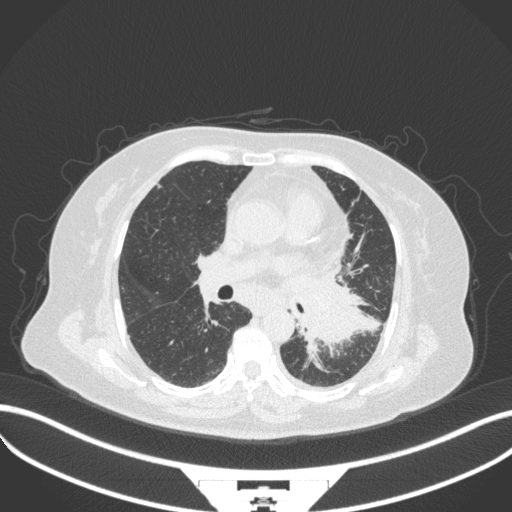
Chest CT, one axial slice. Slice 186 of 328 in the series (ordered by position). Reconstruction kernel B31f. 120 kVp. Lung window (W 1500 / L -600 HU). 1 mm slice thickness. 512 × 512 image matrix, field of view 400 × 400 mm. Female patient, age 69 years. From the clinical record (not read from this slice): clinical TNM (as recorded): T2b N3 M1.
Annotated regions visible in this slice (rectangle marked by the reading radiologist):
- lung tumour (recorded histology: adenocarcinoma): box from (x=293, y=280) to (x=371, y=353) px